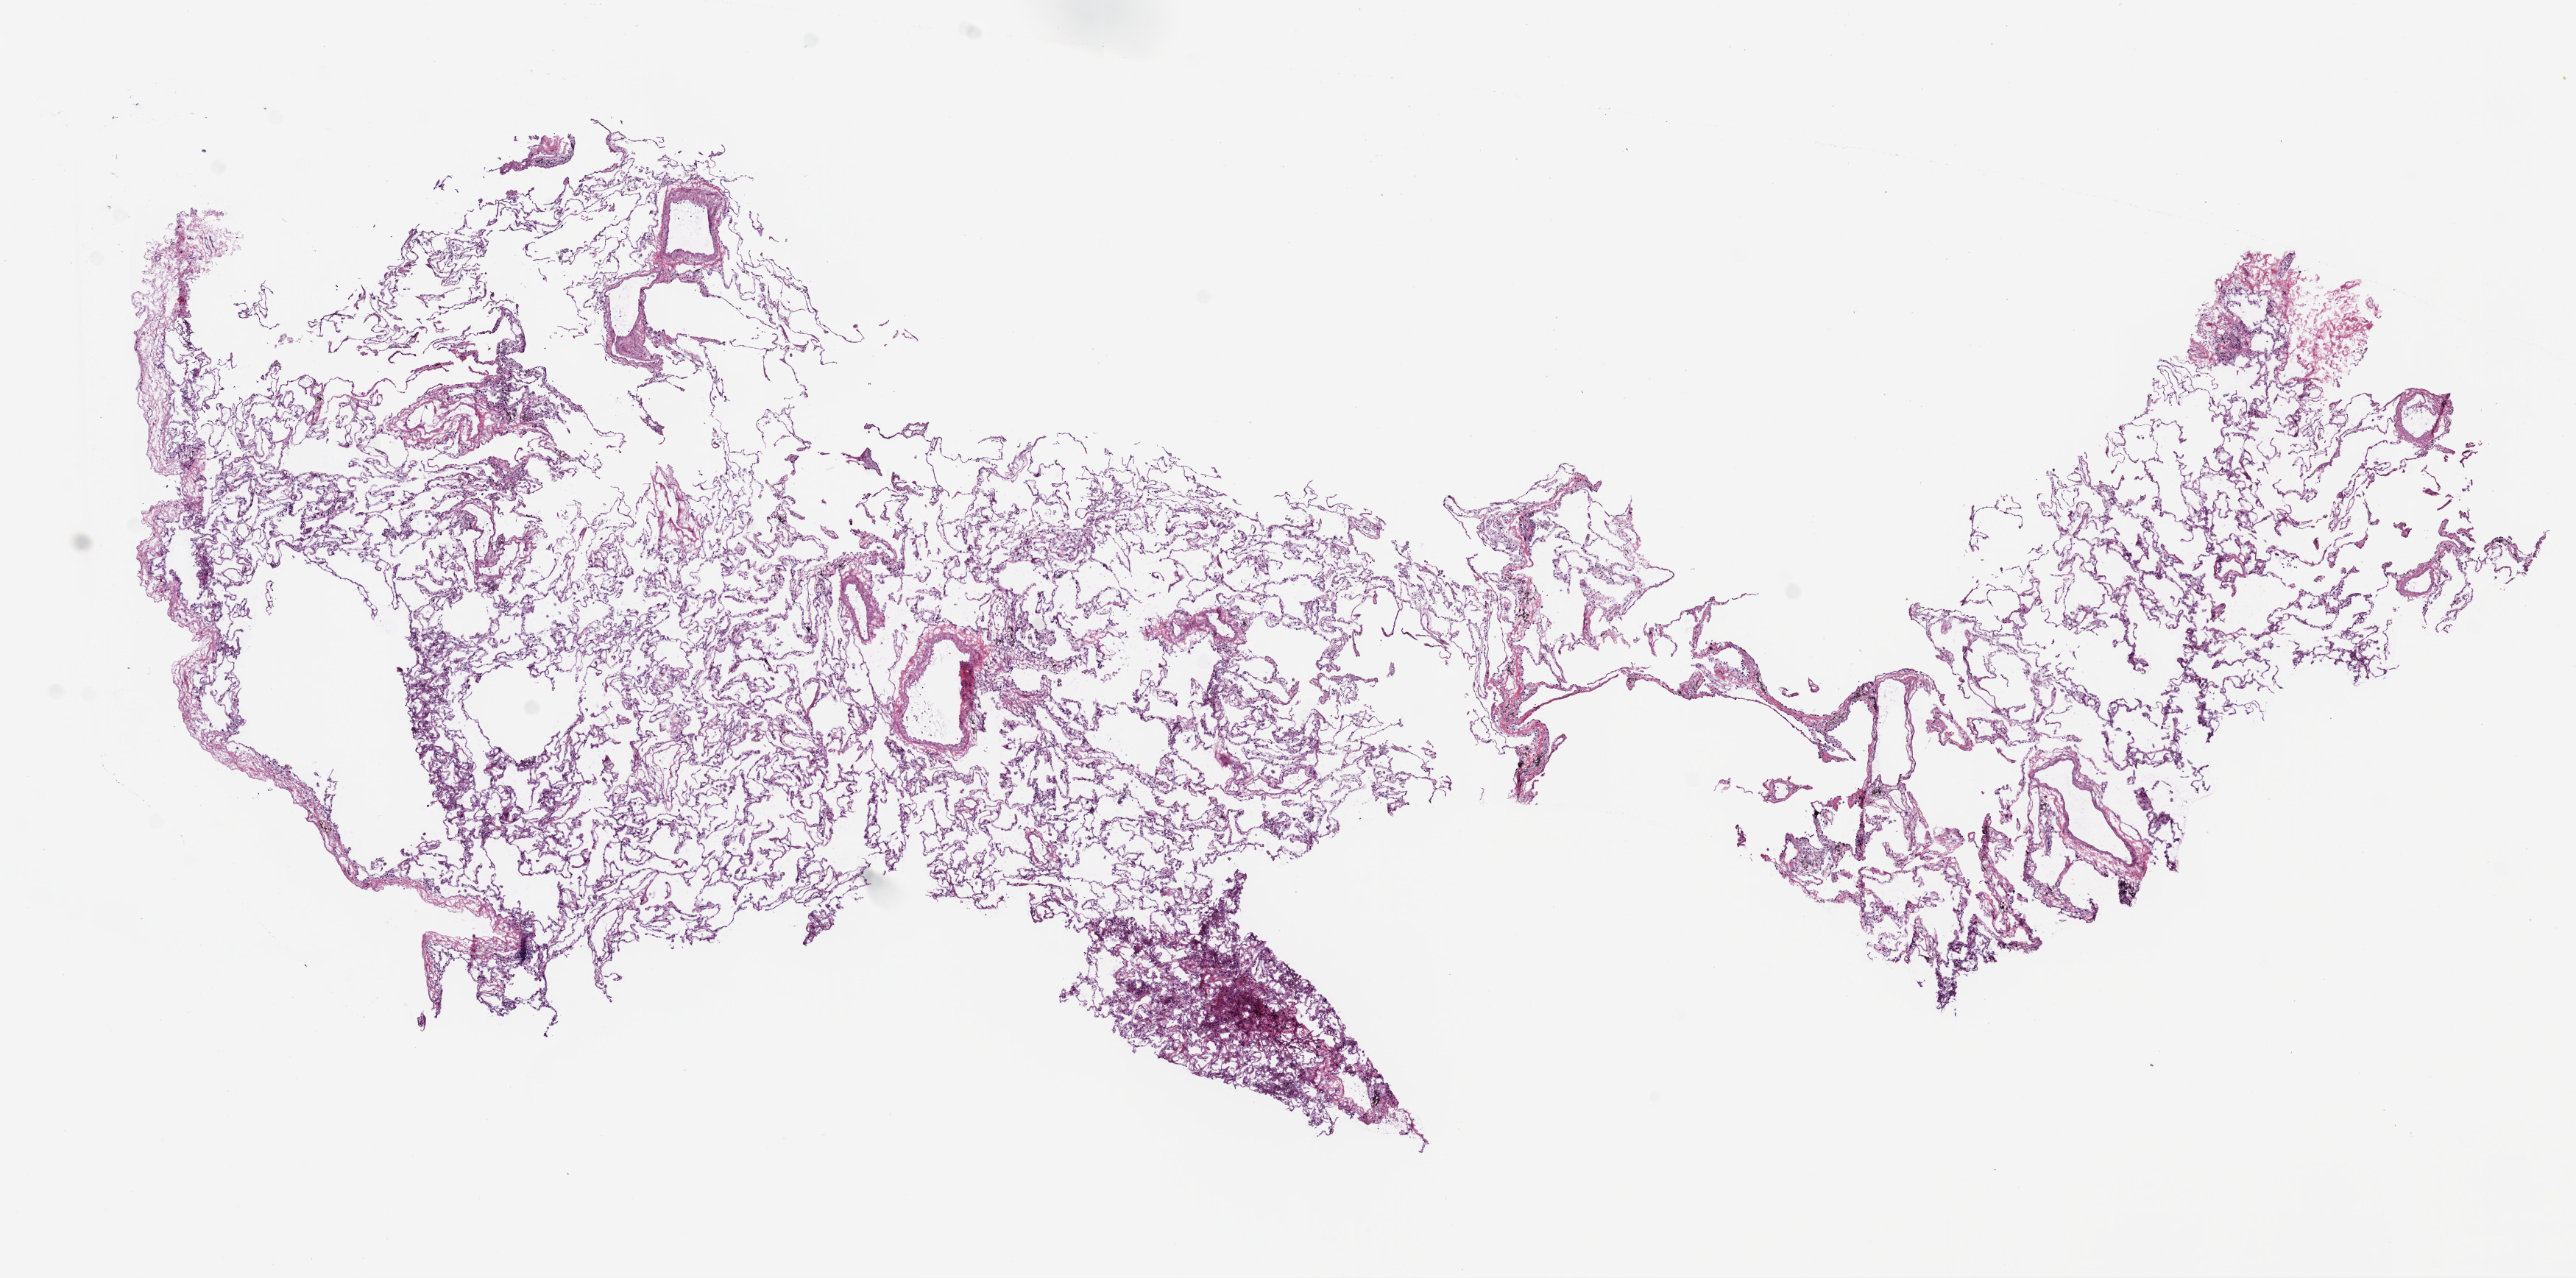
Whole-slide histology image, Hematoxylin and eosin (H&E) stained, whole scanned area (about 14.0 x 7.0 mm, from a 20x scan) shown as a low-resolution overview. Frozen section from the bottom of the tissue portion. Solid tissue normal (non-tumour tissue) sample from the lung. Male, age 81 years at initial diagnosis.
* this section: solid tissue normal (non-tumour) sample from the same patient
* patient diagnosis: Squamous cell carcinoma, NOS